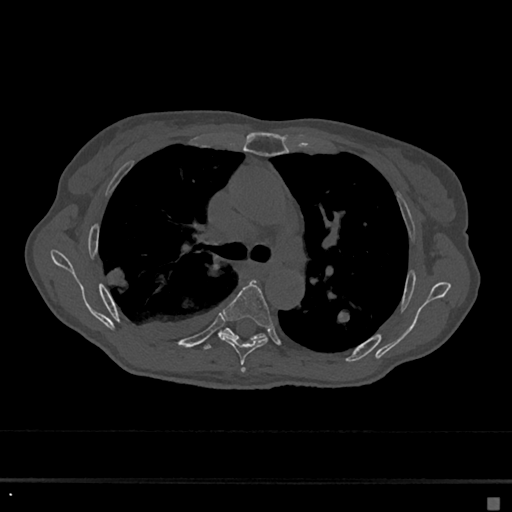
CT including the spine, one axial slice; position 450 of 797 along the scan axis; 120 kVp; bone window (W 1800 / L 400 HU); 0.5 mm slice thickness; 512 × 512 image matrix, field of view 360 × 360 mm. Female patient, age 68 years. From the clinical record (not read from this slice): primary cancer: renal.
Annotated regions visible in this slice (semi-automatic segmentation, software-assisted and operator-edited):
- T5 vertebra: box from (x=221, y=279) to (x=273, y=372) px
- T6 vertebra: (x=204, y=328)–(x=266, y=350)